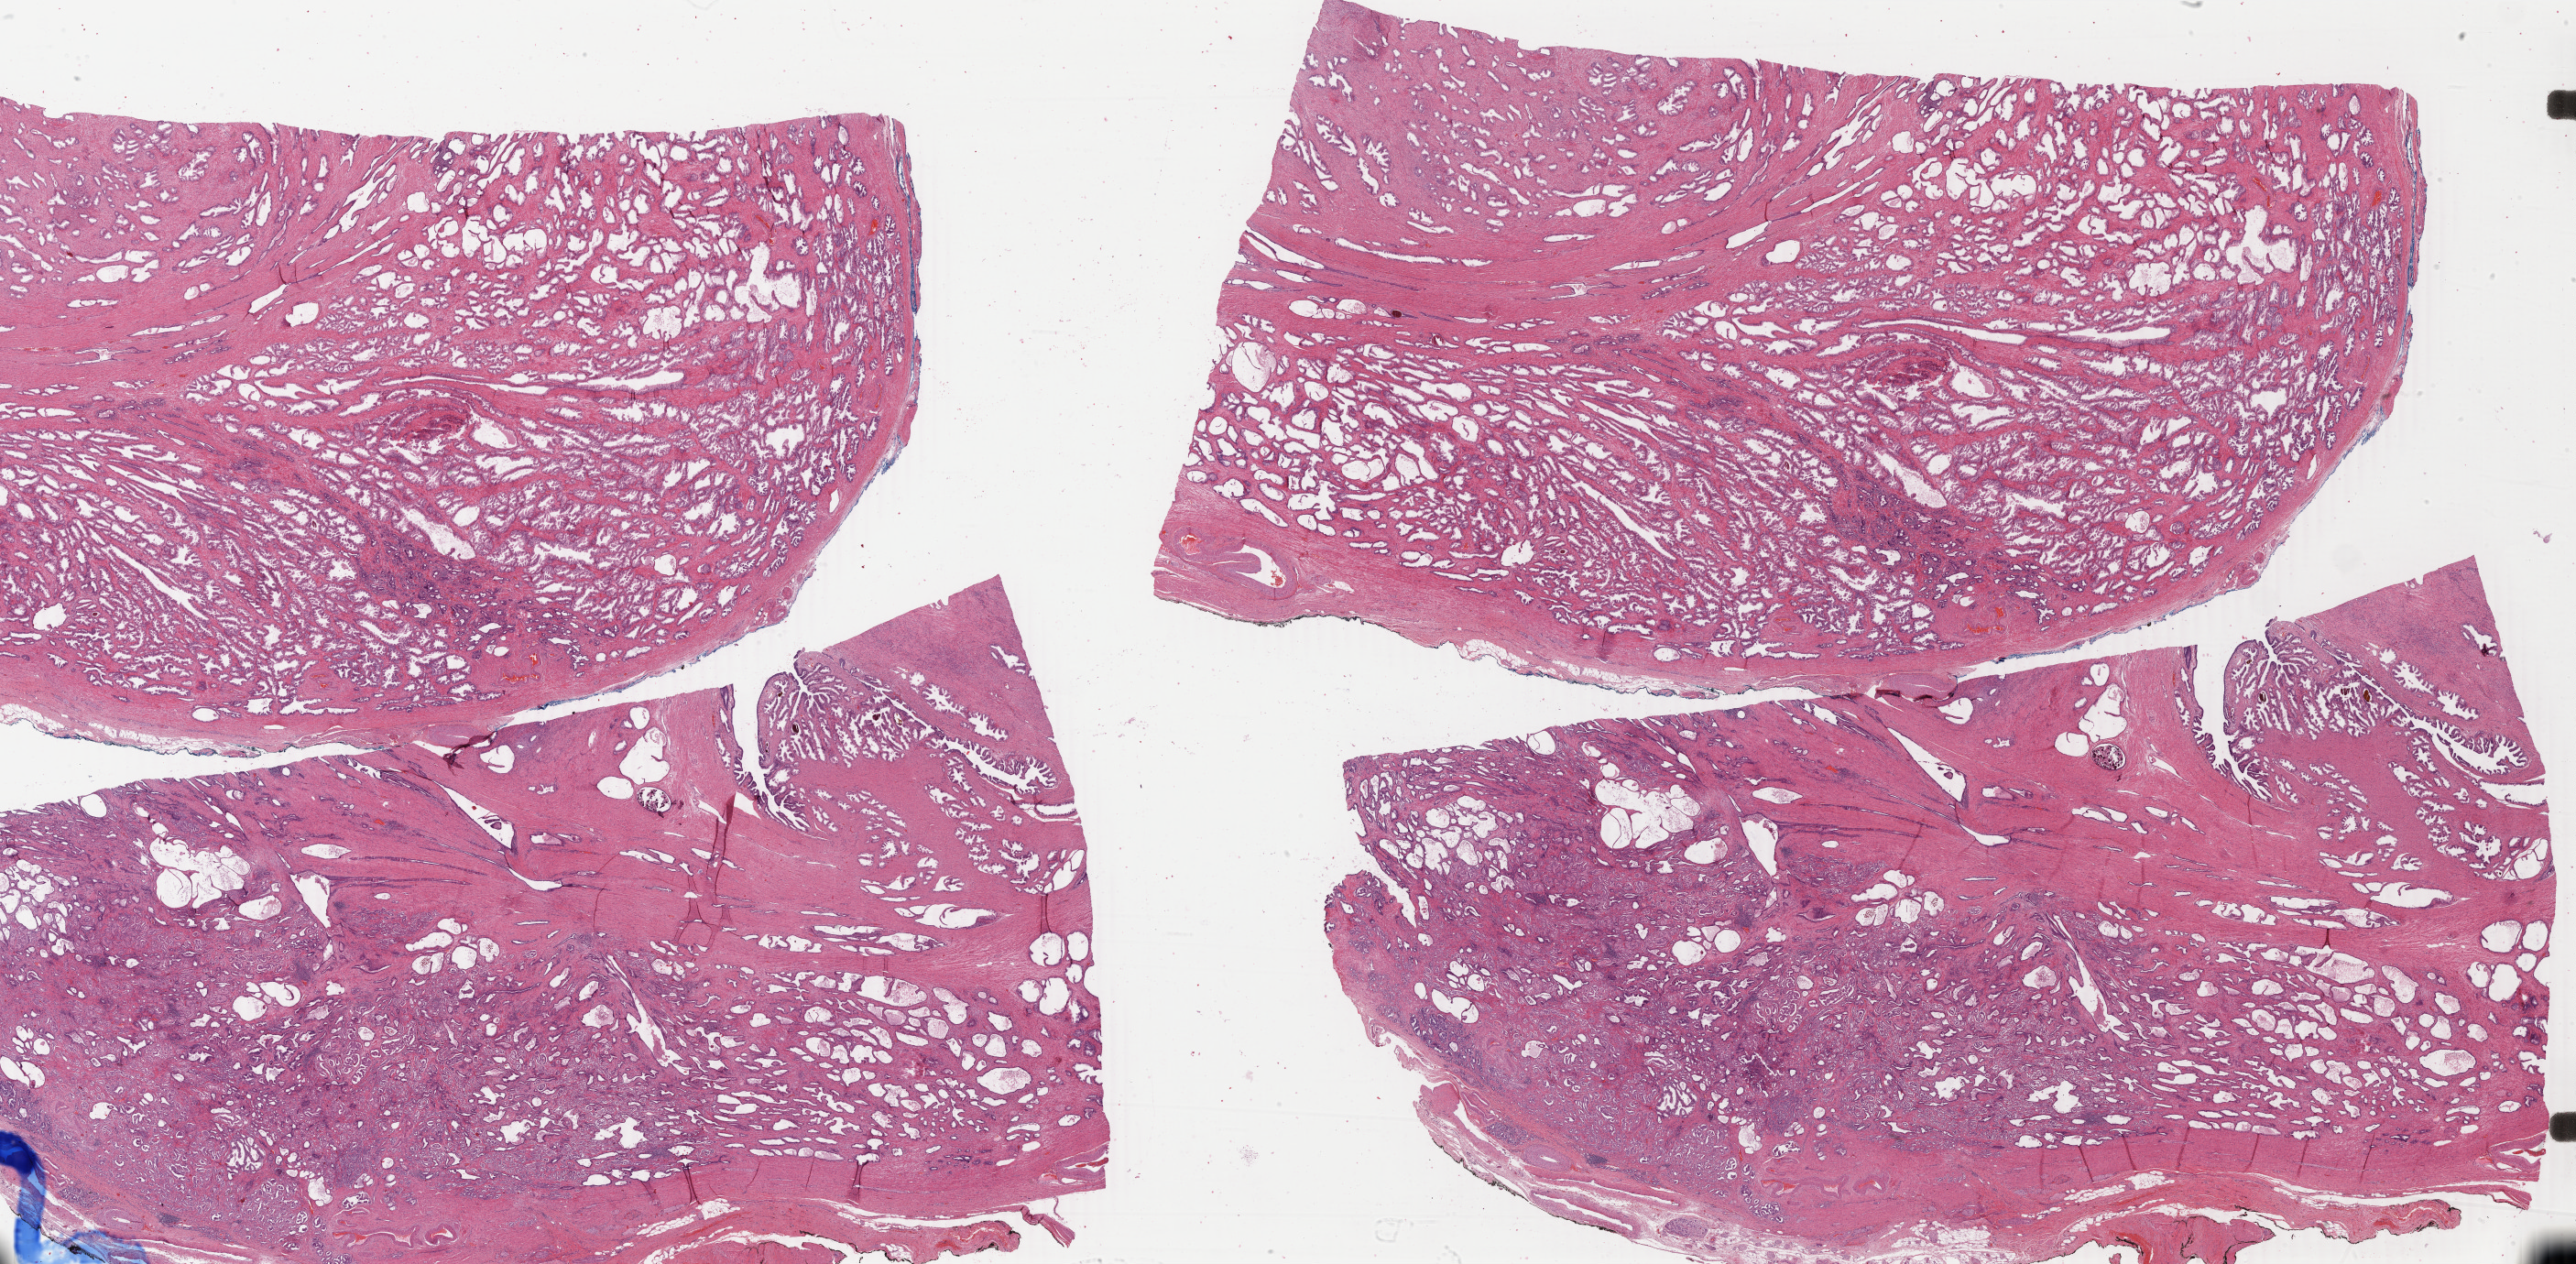
Digitized H&E tissue section (whole slide), whole scanned area (about 44.7 x 22.0 mm, from a 40x scan) shown as a low-resolution overview; FFPE section; sample: primary tumour, prostate. Patient: male, age at initial diagnosis 54 years. Gleason score: 7 (3+4).
- pathologic diagnosis: Adenocarcinoma, NOS
- lymph nodes positive (case pathology): 0 of 1 examined